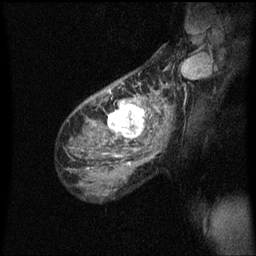
Breast MRI (dynamic contrast-enhanced), one sagittal slice; slice 39 of 60 in the series (ordered by position); dynamic contrast-enhanced series, image 2 of 3 at this slice position (ordered by acquisition); 1.5 T; TE 4.2 ms, TR 8.4 ms; 2 mm slice thickness; 256 × 256 image matrix, field of view 200 × 200 mm. Patient: female, 49 years.
Annotated regions visible in this slice (semi-automatic segmentation, software-assisted and operator-edited):
- analysis volume of interest (the breast-tissue region the enhancement analysis was run in; not a lesion): bounding box (x1, y1, x2, y2) in pixels: (103, 90, 157, 151)
- tumour enhancement mask (voxels above the 70 % enhancement threshold inside the analysis volume of interest): (108, 90, 157, 151)